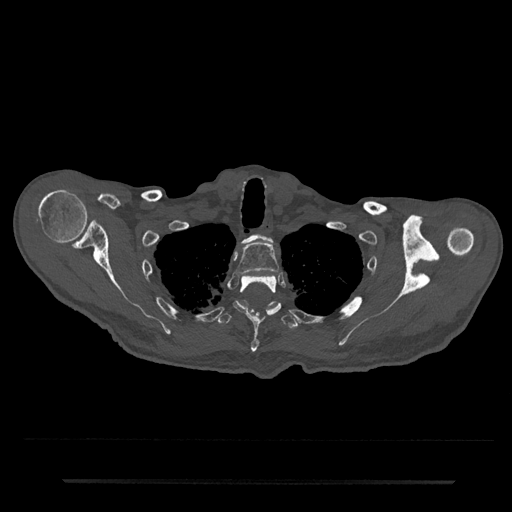
CT including the spine, one axial slice. Position 660 of 797 along the scan axis. Bone window (W 1800 / L 400 HU). 512 × 512 image matrix, field of view 427 × 427 mm. Male patient, age 74 years. From the clinical record (not read from this slice): primary cancer: prostate.
Outlined on this slice (semi-automatically segmented with operator editing):
- T1 vertebra: bounding box [x1, y1, x2, y2] px = [243, 234, 273, 243]
- T2 vertebra: [236, 242, 279, 275]
- T3 vertebra: [233, 275, 282, 353]
- T4 vertebra: [217, 300, 299, 329]